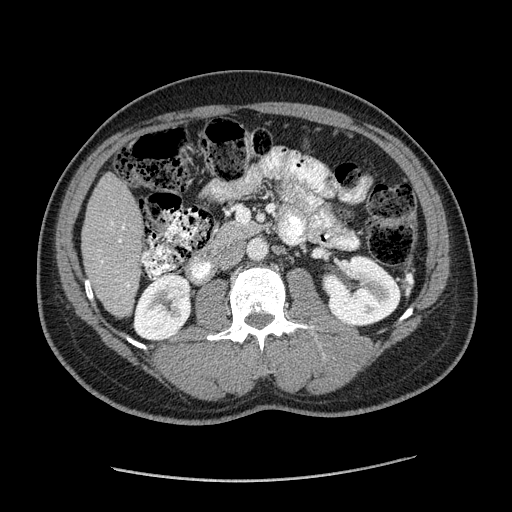
Contrast-enhanced abdominal CT (liver protocol), one axial slice. Slice 55 of 182 in the series (ordered by position). Reconstruction kernel STANDARD. Soft-tissue window (W 400 / L 40 HU). 2.5 mm slice thickness. 512 × 512 image matrix, field of view 400 × 400 mm. From the clinical record (not read from this slice): diagnosis: hepatocellular carcinoma (patient treated with transarterial chemoembolisation; whether this scan precedes or follows treatment is not stated here); TNM stage (as recorded): Stage-I; Child-Pugh class: A; tumour differentiation: well differentiated; tumour size: 3.1 cm.
Outlined on this slice (semi-automatic segmentation, software-assisted and operator-edited):
- liver parenchyma outside the tumour (the mass and vessels are separate outlines, so this box may not span the whole liver): bounding box [x1, y1, x2, y2] px = [82, 173, 142, 316]
- liver vessels: [101, 222, 129, 286]